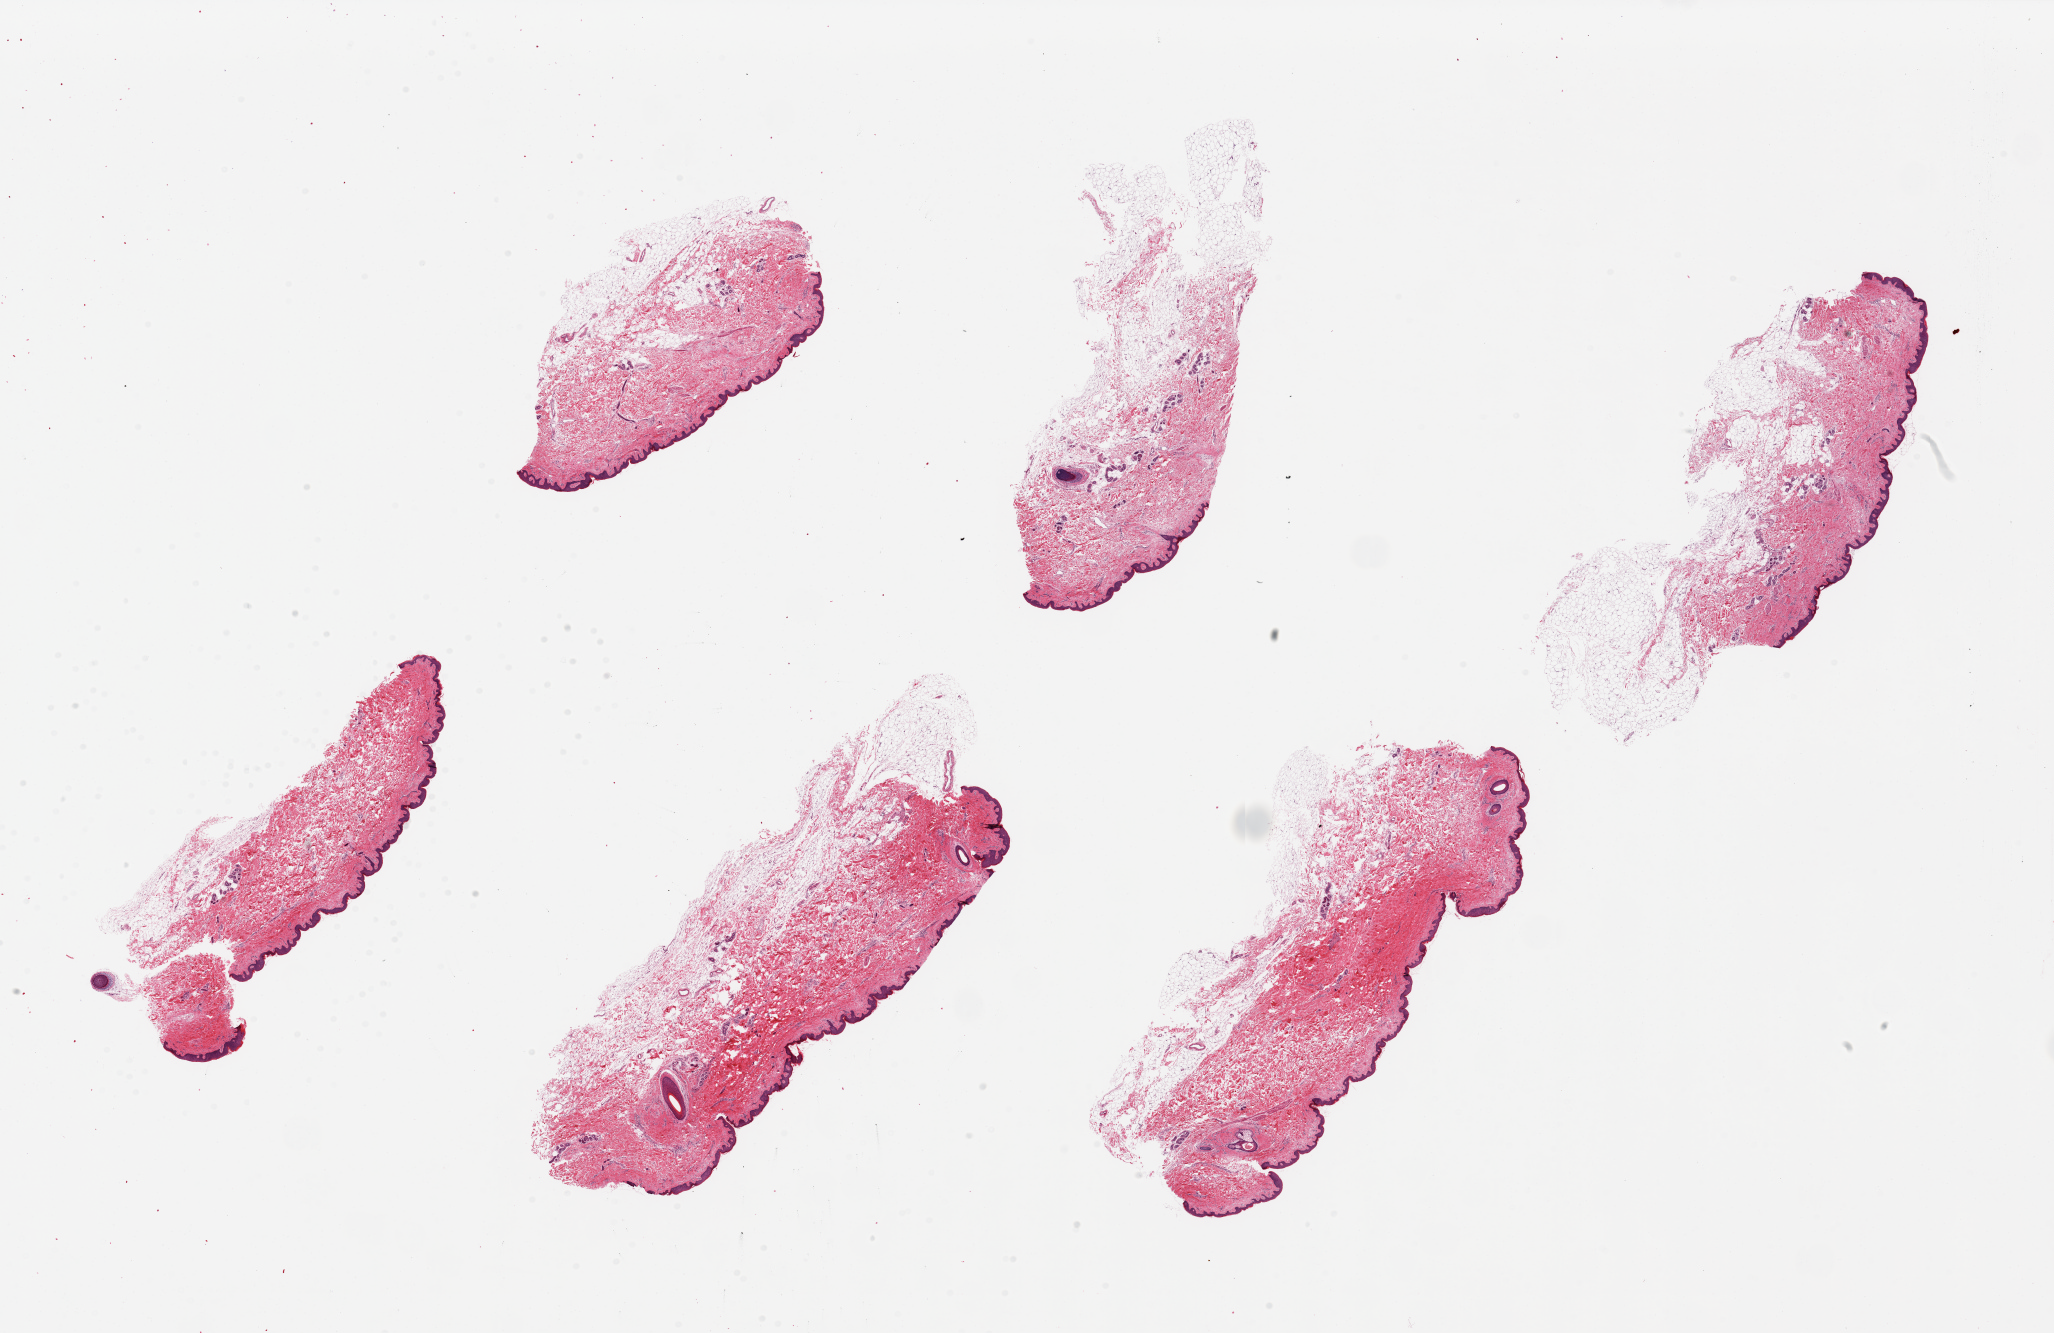
Digitized hematoxylin and eosin (H&E)-stained section, low-resolution overview of the scanned area, about 32.5 x 21.1 mm (slide scanned at 20x); PAXgene-fixed, paraffin-embedded tissue; target tissue: skin of suprapubic region; donor tissue sample. Donor sex: female.
Reviewer comment on this tissue sample: 6 pieces, up to 10x3.5mm; Subcutaneous adipose up to 1 mm on all.